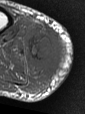
MRI of an extremity soft-tissue mass, one axial slice; position 16 of 47 along the scan axis; MR volume resampled by the dataset authors to the PET/CT grid (not the native acquisition matrix); 3.27 mm slice thickness; 85 × 114 image matrix. Male patient. Case-level facts recorded for this patient, not image findings: histological type: pleiomorphic liposarcoma; grade: high; site of the primary tumour: right calf.
Outlined on this slice (expert contour drawn on MRI and transferred to this co-registered scan by the dataset authors):
- gross tumour volume including surrounding oedema: bounding box (x1, y1, x2, y2) in pixels: (22, 21, 66, 92)
- gross tumour volume (mass): (26, 30, 66, 69)